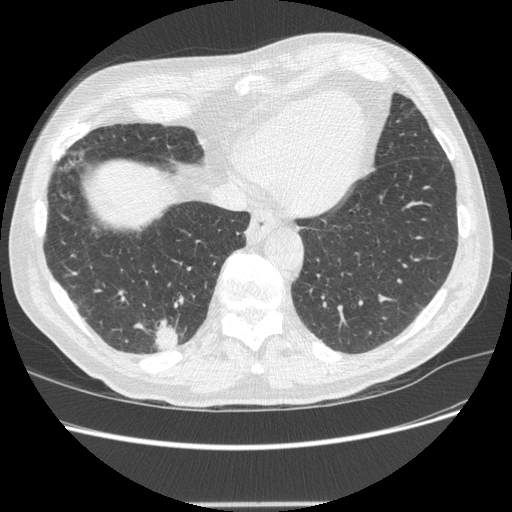
Low-dose screening chest CT, one axial slice; slice 61 of 245 in the series (ordered by position); reconstruction kernel STANDARD; 120 kVp; lung window (W 1500 / L -600 HU); 512 × 512 image matrix, field of view 372 × 372 mm.
Annotated regions visible in this slice (manually delineated by an expert):
- lesion 1 (tumor, lower lobe of right lung): bounding box <154,320,179,351> (left, top, right, bottom; pixels)